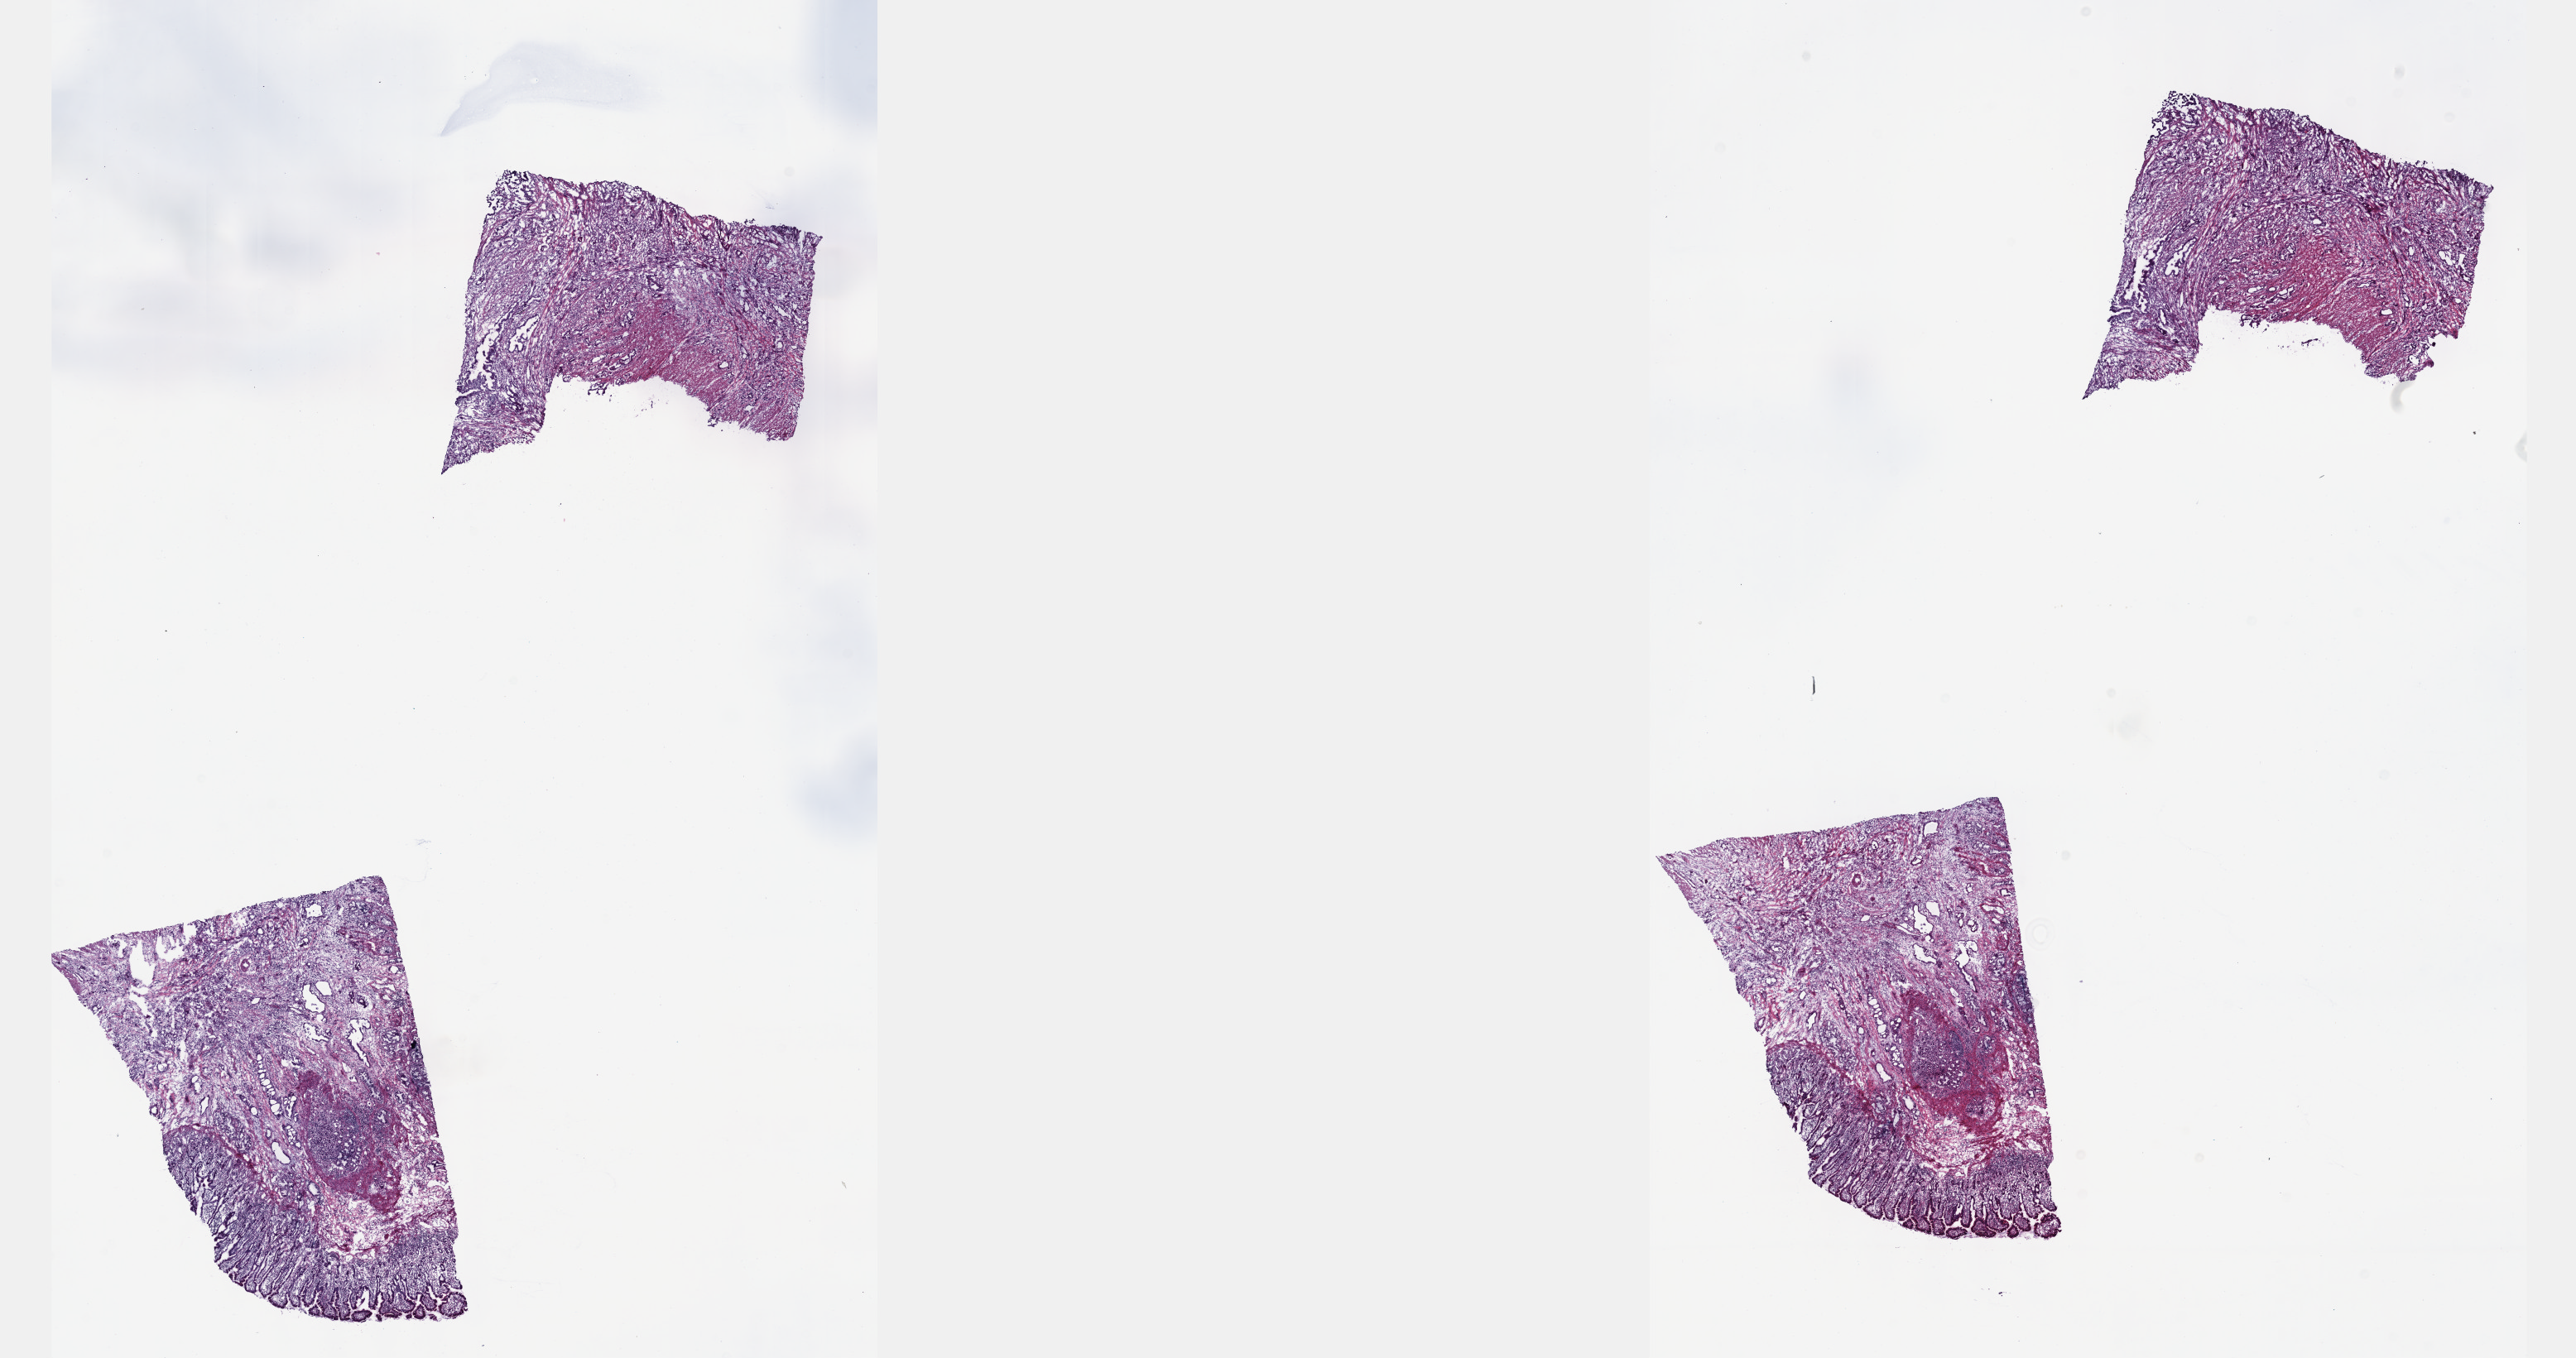
Whole-slide histology image, H&E-stained, whole scanned area (about 25.1 x 13.3 mm, acquisition: 40x scan) shown as a low-resolution overview. Frozen section. Sample: primary tumour, pancreas. Patient: male, age at initial diagnosis 45 years. Histologic grade: G2 (moderately differentiated). Slide review estimates, as recorded: tumour cells 70%, tumour nuclei 70%, normal cells 5%, stromal cells 25%, necrosis 0%. Infiltration values recorded for this section: lymphocyte infiltration 40%, monocyte infiltration 20%, neutrophil infiltration 20%.
Diagnosis: Infiltrating duct carcinoma, NOS (head of pancreas). AJCC pathologic stage: IIB (7th edition).